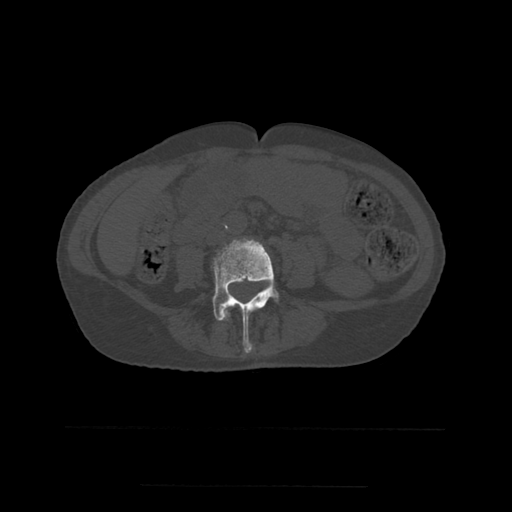
CT including the spine, one axial slice. Slice 169 of 544 in the series (ordered by position). Bone window (W 1800 / L 400 HU). 1.25 mm slice thickness. 512 × 512 image matrix, field of view 350 × 350 mm. Patient age 58 years. Case-level facts recorded for this patient, not image findings: primary cancer: lung.
Annotated regions visible in this slice (semi-automatically segmented with operator editing):
- L3 vertebra: bounding box (x1, y1, x2, y2) in pixels: (223, 306, 260, 321)
- L4 vertebra: (210, 238, 279, 353)